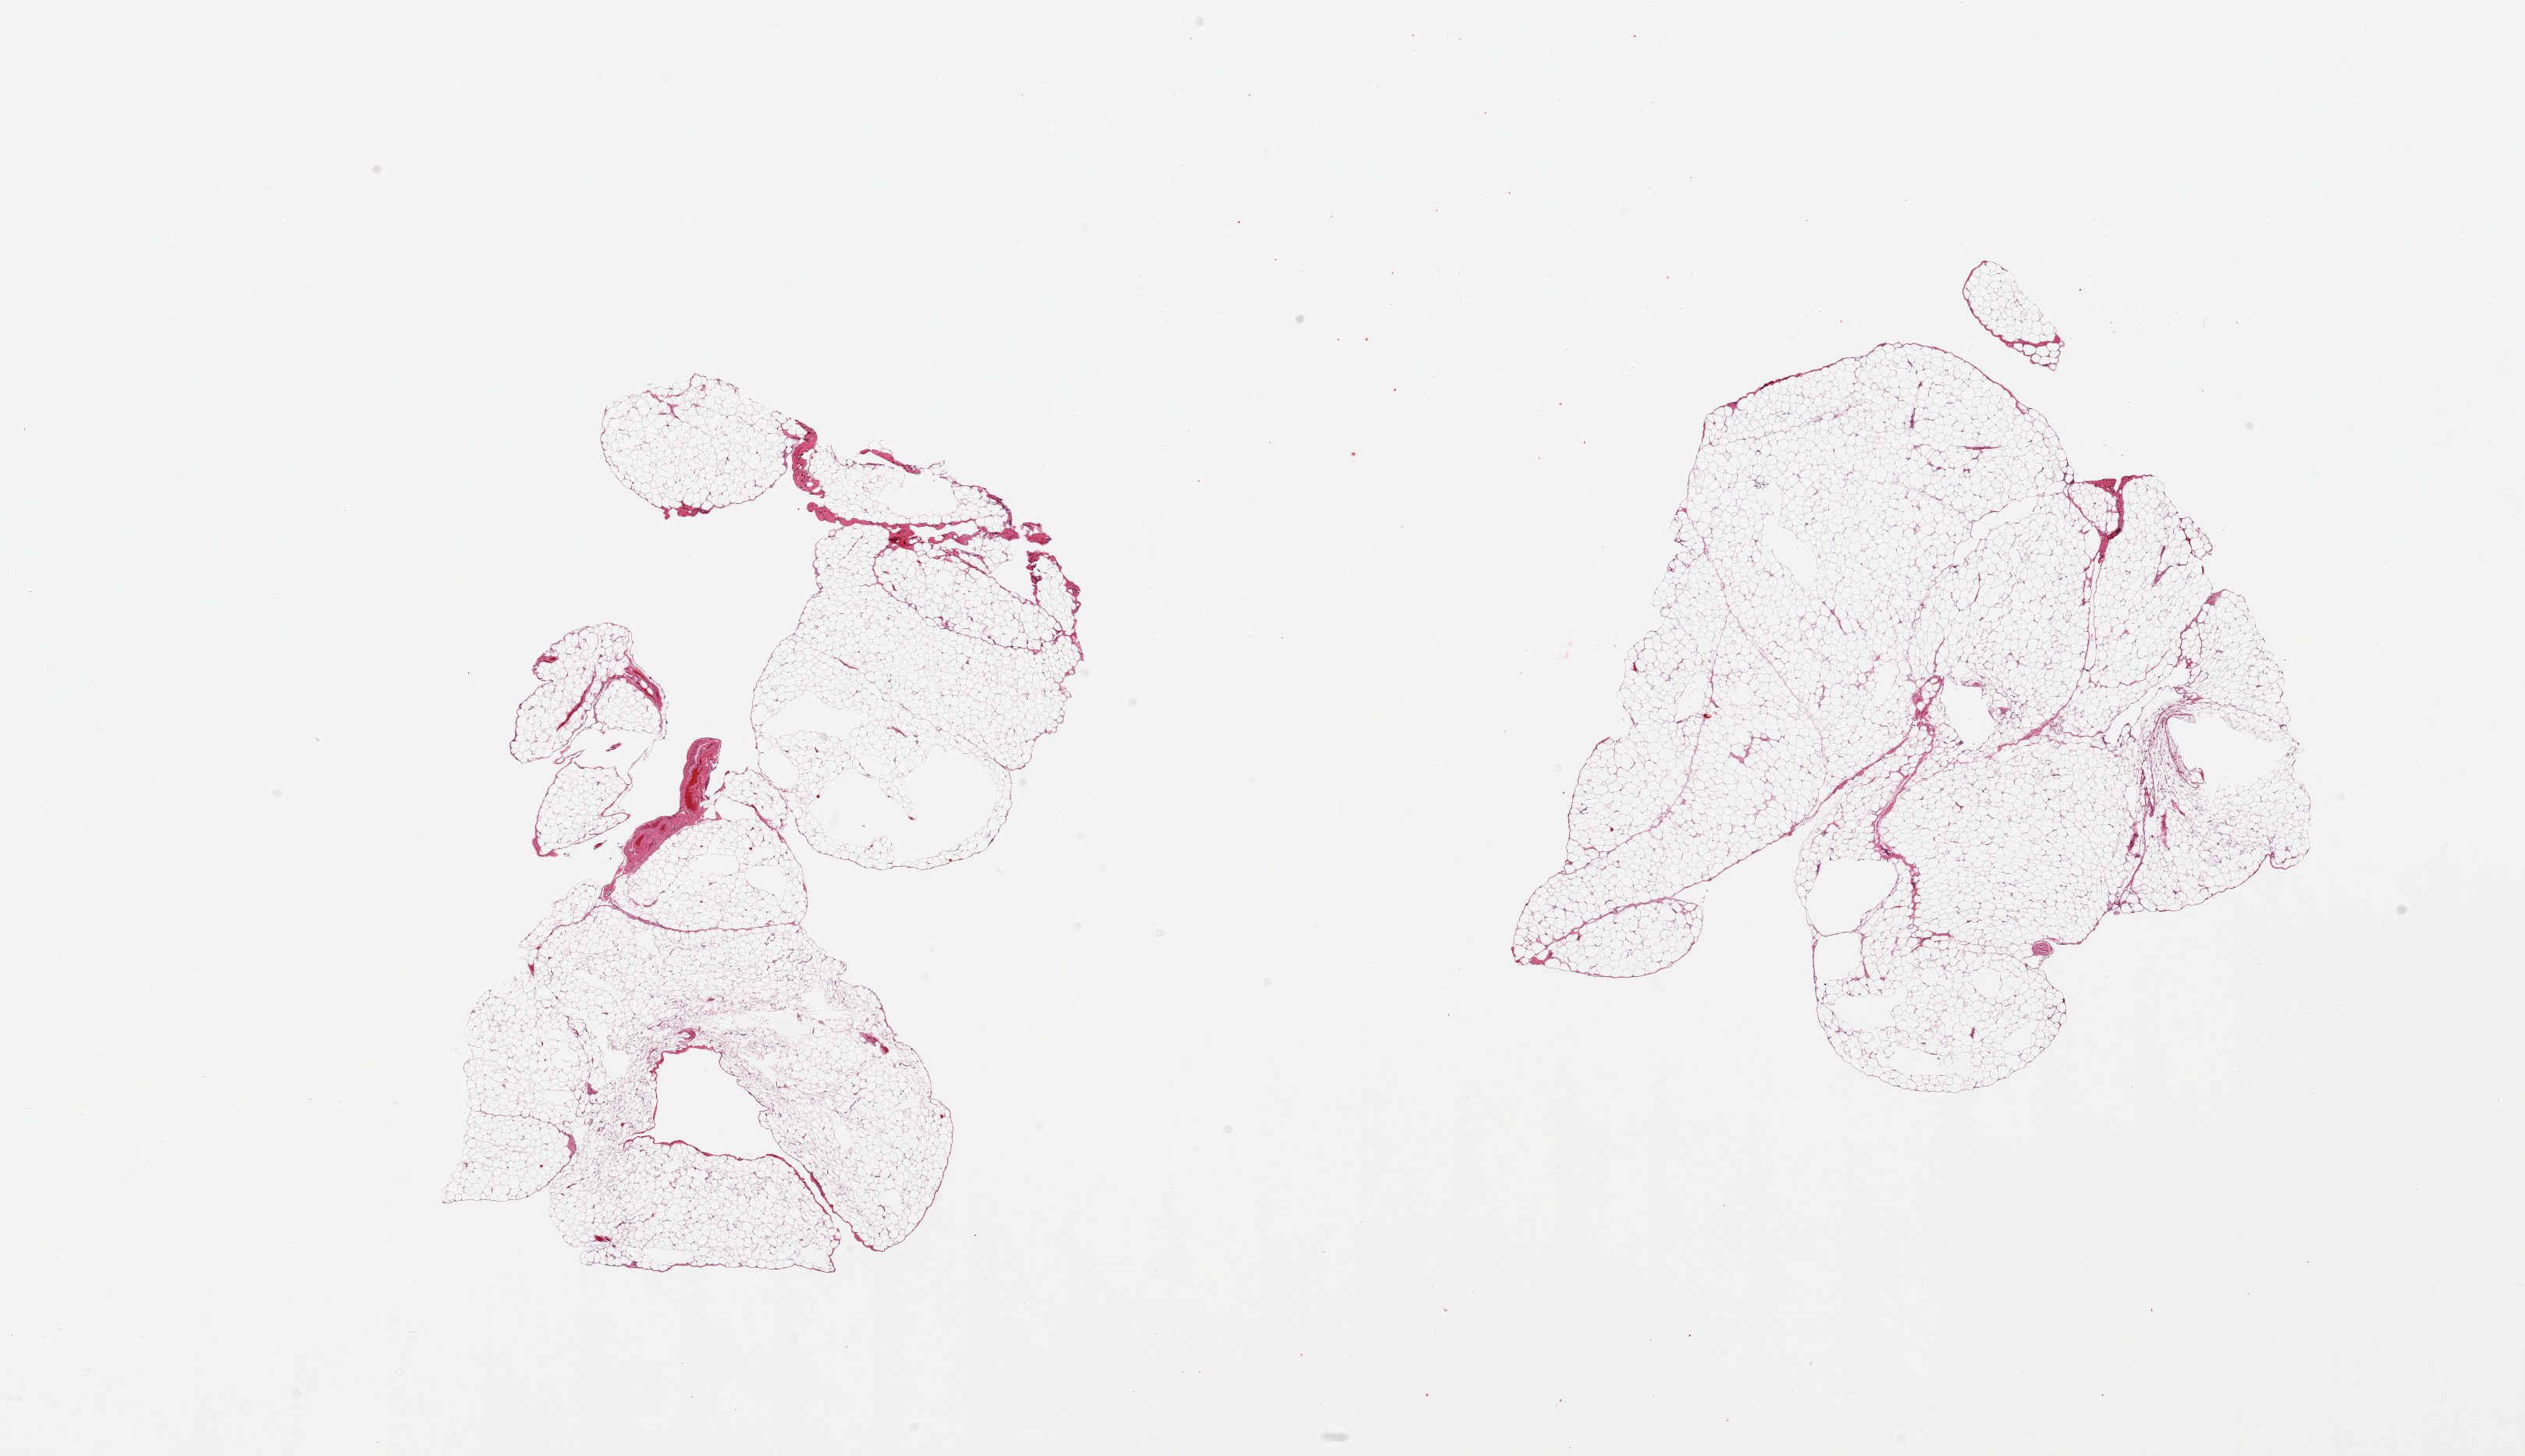
Digitized H&E-stained section, brightfield, low-resolution overview of the scanned area, about 25.6 x 14.8 mm. PAXgene-fixed paraffin-embedded (PFPE) section. Sampled site (target tissue): omentum. Tissue donor sample. Donor sex: male.
* review note (as recorded): 2 pieces; mature adipose tissue